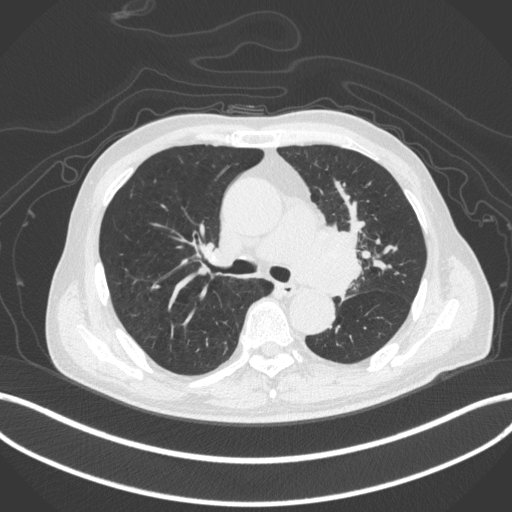
Chest CT, one axial slice; position 274 of 420 along the scan axis; lung window (W 1500 / L -600 HU); 1 mm slice thickness; 512 × 512 image matrix, field of view 400 × 400 mm. Male patient, age 77 years. Case-level facts recorded for this patient, not image findings: clinical TNM (as recorded): T3 N1 M0.
Structures marked on this image (bounding box drawn by a radiologist):
- lung tumour (recorded histology: adenocarcinoma): bounding box <290,220,362,305> (left, top, right, bottom; pixels)